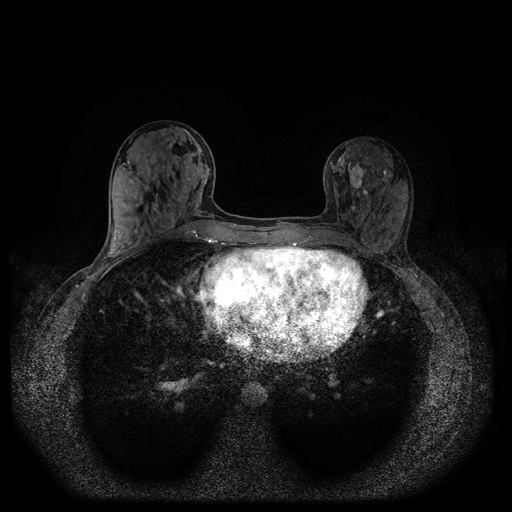
Breast MRI (dynamic contrast-enhanced, multi-phase), one axial slice. Dynamic contrast-enhanced series, time point 2 of 5 at this slice position (early post-contrast). 1.5 T. TE 2.6 ms, TR 5.4 ms. 2 mm slice thickness. 512 × 512 image matrix, field of view 340 × 340 mm. Female patient, age 32 years.
Outlined on this slice (semi-automatically segmented with operator editing):
- breast lesion (labelled benign in the annotation): box from (x=349, y=165) to (x=364, y=191) px